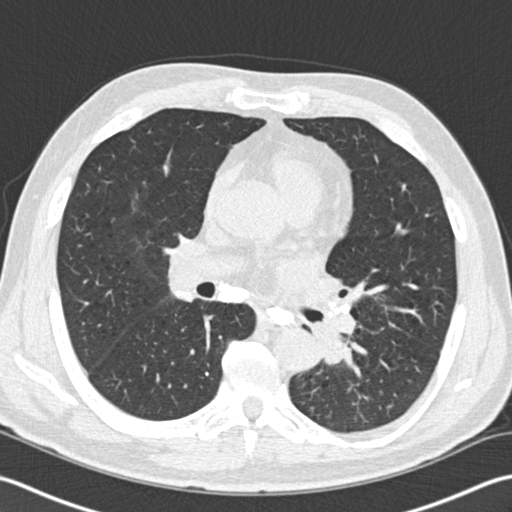
Low-dose screening chest CT, one axial slice. Position 95 of 170 along the scan axis. Reconstruction kernel B30f. 120 kVp. Lung window (W 1500 / L -600 HU). 2 mm slice thickness. 512 × 512 image matrix, field of view 350 × 350 mm.
Annotated regions visible in this slice (manually delineated by an expert):
- lesion 1 (tumor, lower lobe of left lung): bounding box (x1, y1, x2, y2) in pixels: (314, 322, 352, 365)